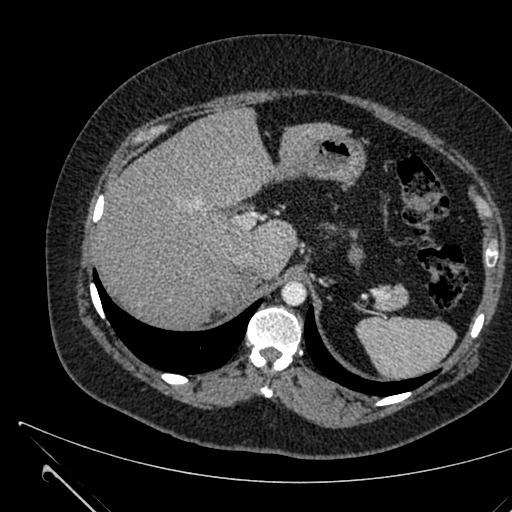
Contrast-enhanced abdominal CT, one axial slice. Intravenous contrast given. Soft-tissue window (W 400 / L 40 HU). 1 mm slice thickness. 512 × 512 image matrix, field of view 376 × 376 mm. Patient: female, 36 years. From the clinical record (not read from this slice): diagnosis: adrenocortical carcinoma; tumour side: right adrenal; tumour size at pathology: 10 cm; Ki-67 index: 20 %; stage (as recorded): 4.
Outlined on this slice (semi-automatic segmentation, software-assisted and operator-edited):
- mass: bounding box <217,273,256,309> (left, top, right, bottom; pixels)